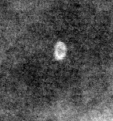
Region of interest cut from a scanned film mammogram (one marked finding); right breast; MLO view.
- Finding: calcifications, morphology lucent center; BI-RADS assessment category 2; subtlety rating 3 on a 1 (subtle) to 5 (obvious) scale; benign; no additional work-up was recommended (benign without callback).